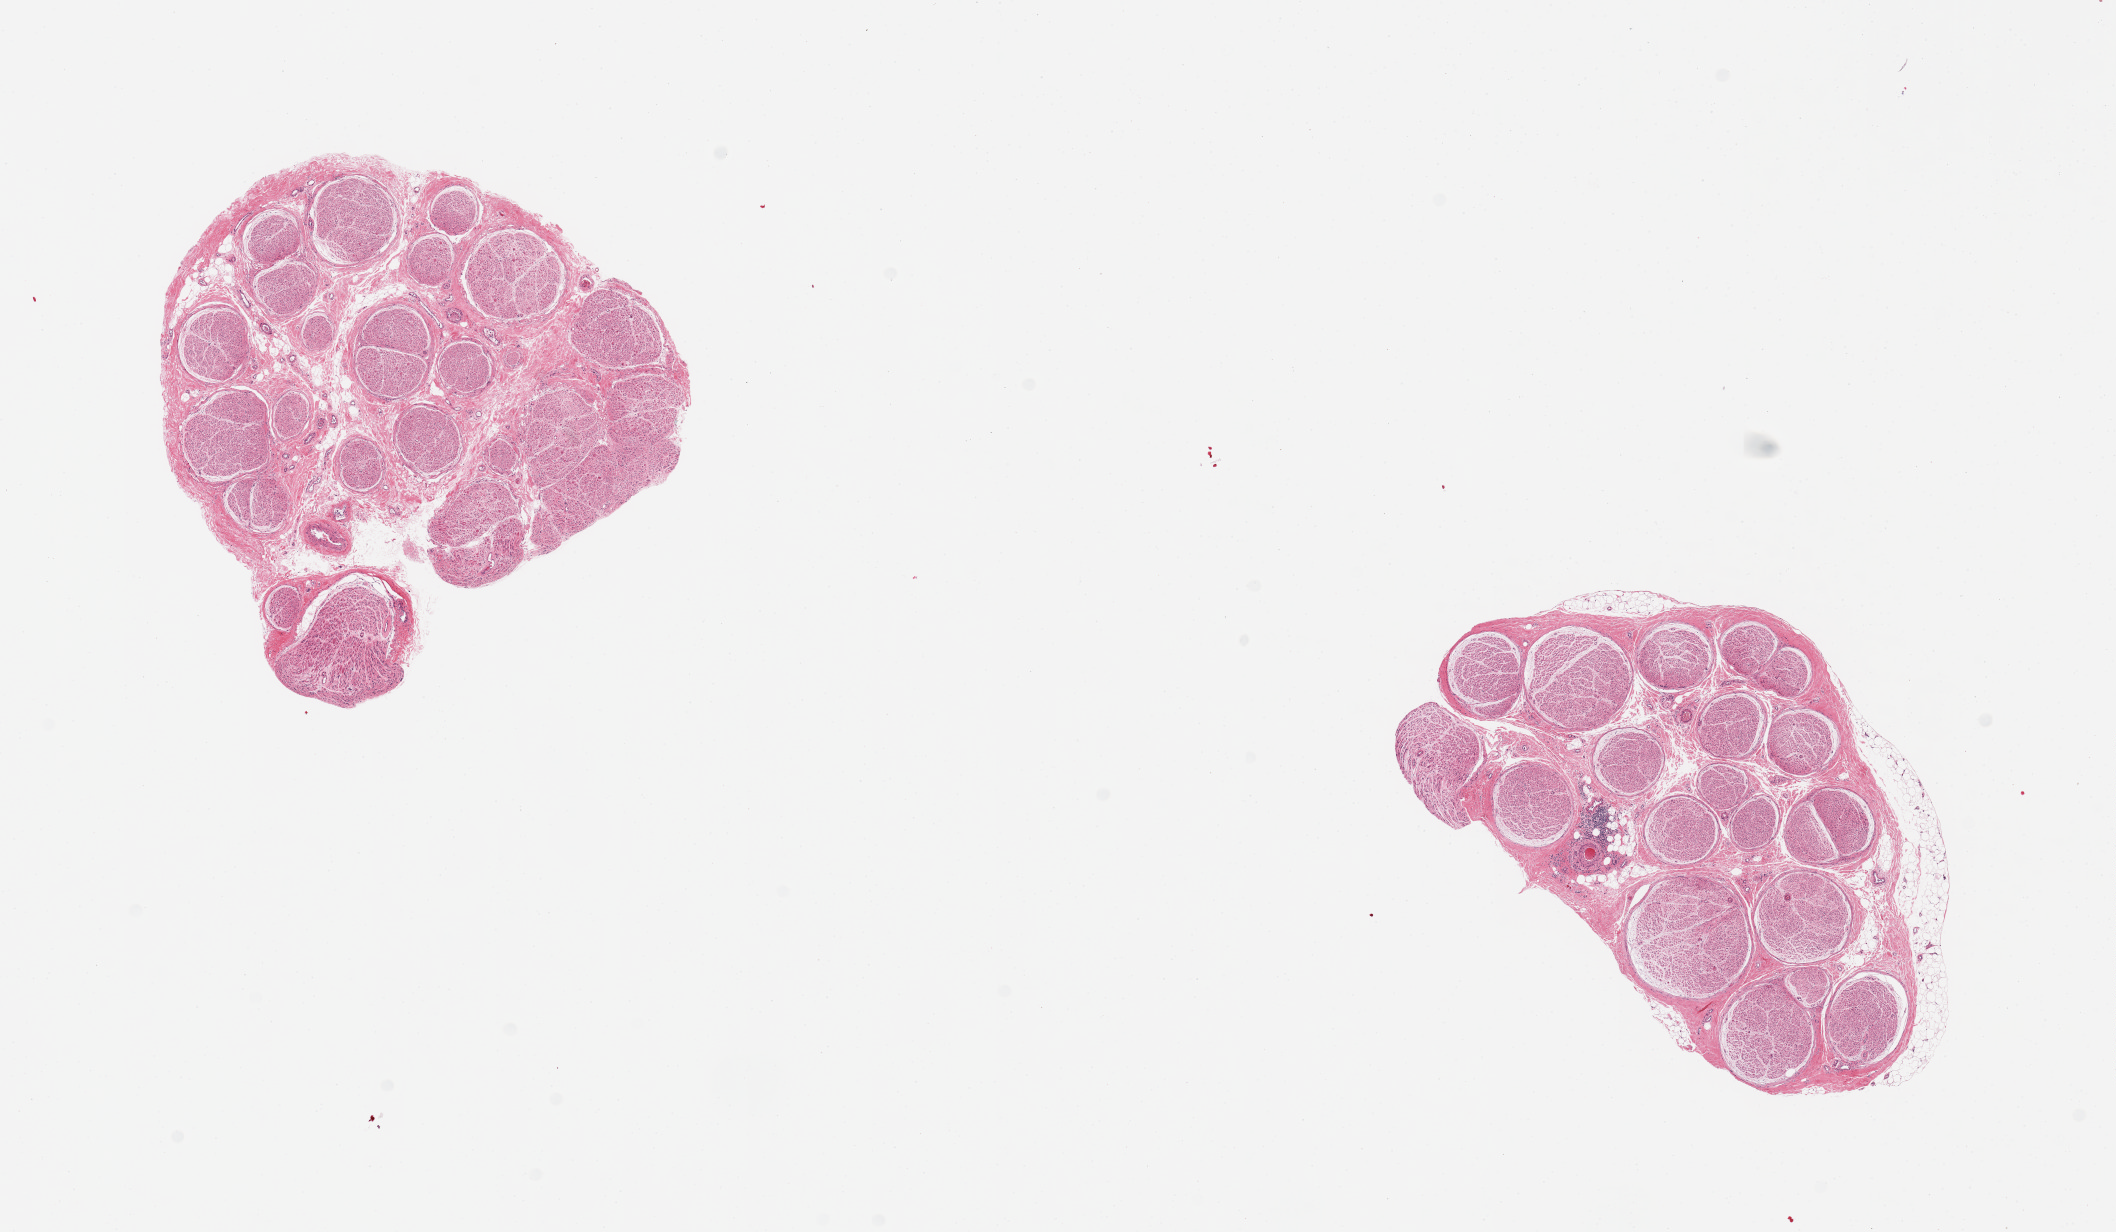
Digitized haematoxylin and eosin-stained section, brightfield — whole scanned area (about 16.7 x 9.7 mm) shown as a low-resolution overview, PAXgene-fixed, paraffin-embedded tissue, target tissue: tibial nerve, donor tissue sample.
Reviewer comment on this tissue sample: 2 pieces, good clean specimens; minute nubbin of adherent fat on one, ~0.3mm.